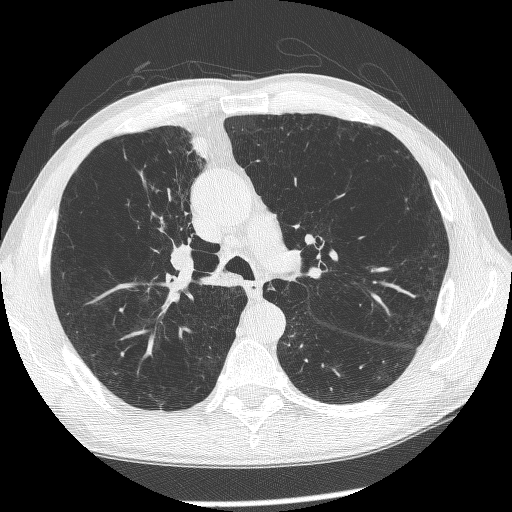
Low-dose screening chest CT, axial slice, first (baseline) screen, lung window (W 1500 / L -600 HU), lung (sharp) reconstruction kernel (BONE), slice 161 of 266 in the series, 512 × 512 image matrix. Male participant, aged 60 years at enrolment. Current smoker at enrolment.
Expert-annotated lung lesion, box from (x=144, y=213) to (x=227, y=305) px. Screening reader's record for this exam (one nodule recorded; not confirmed to be the boxed lesion): non-calcified nodule or mass ≥4 mm, right upper lobe, 12 × 8 mm, spiculated (stellate) margins, mixed attenuation. Official screen result: positive, change unspecified: nodule(s) >= 4 mm or enlarging nodule(s), mass(es), or other non-specific abnormalities suspicious for lung cancer.